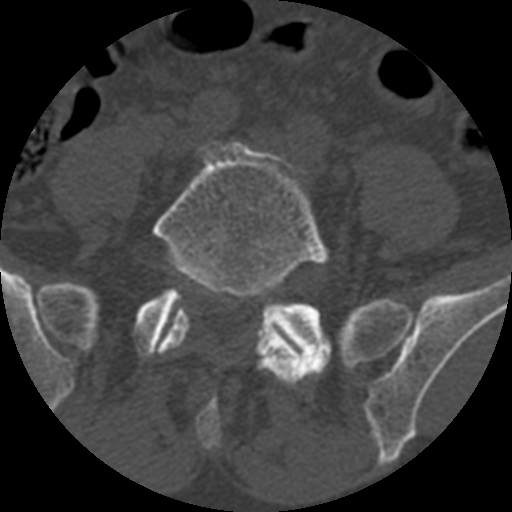
CT including the spine, one axial slice. Position 250 of 399 along the scan axis. Bone window (W 1800 / L 400 HU). 1.25 mm slice thickness. 512 × 512 image matrix. Patient age 71 years. Case-level facts recorded for this patient, not image findings: primary cancer: prostate.
Outlined on this slice (semi-automatically segmented with operator editing):
- L5 vertebra: bounding box <152,142,332,387> (left, top, right, bottom; pixels)